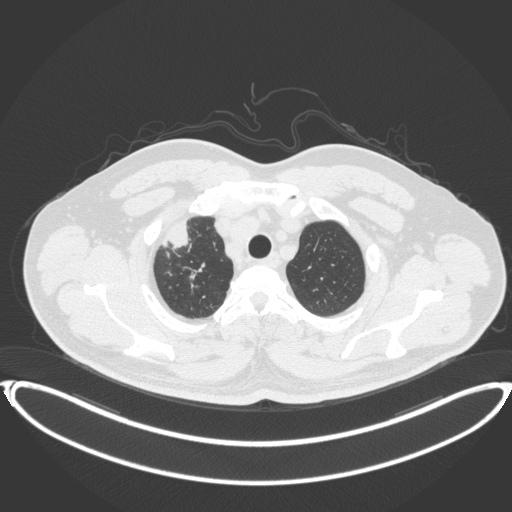
Chest CT, one axial slice; lung window (W 1500 / L -600 HU); 512 × 512 image matrix. Patient: male, 53 years. Case-level facts recorded for this patient, not image findings: clinical TNM (as recorded): T2a N0 M0.
Structures marked on this image (bounding box drawn by a radiologist):
- lung tumour (recorded histology: adenocarcinoma): bounding box (x1, y1, x2, y2) in pixels: (165, 221, 201, 255)